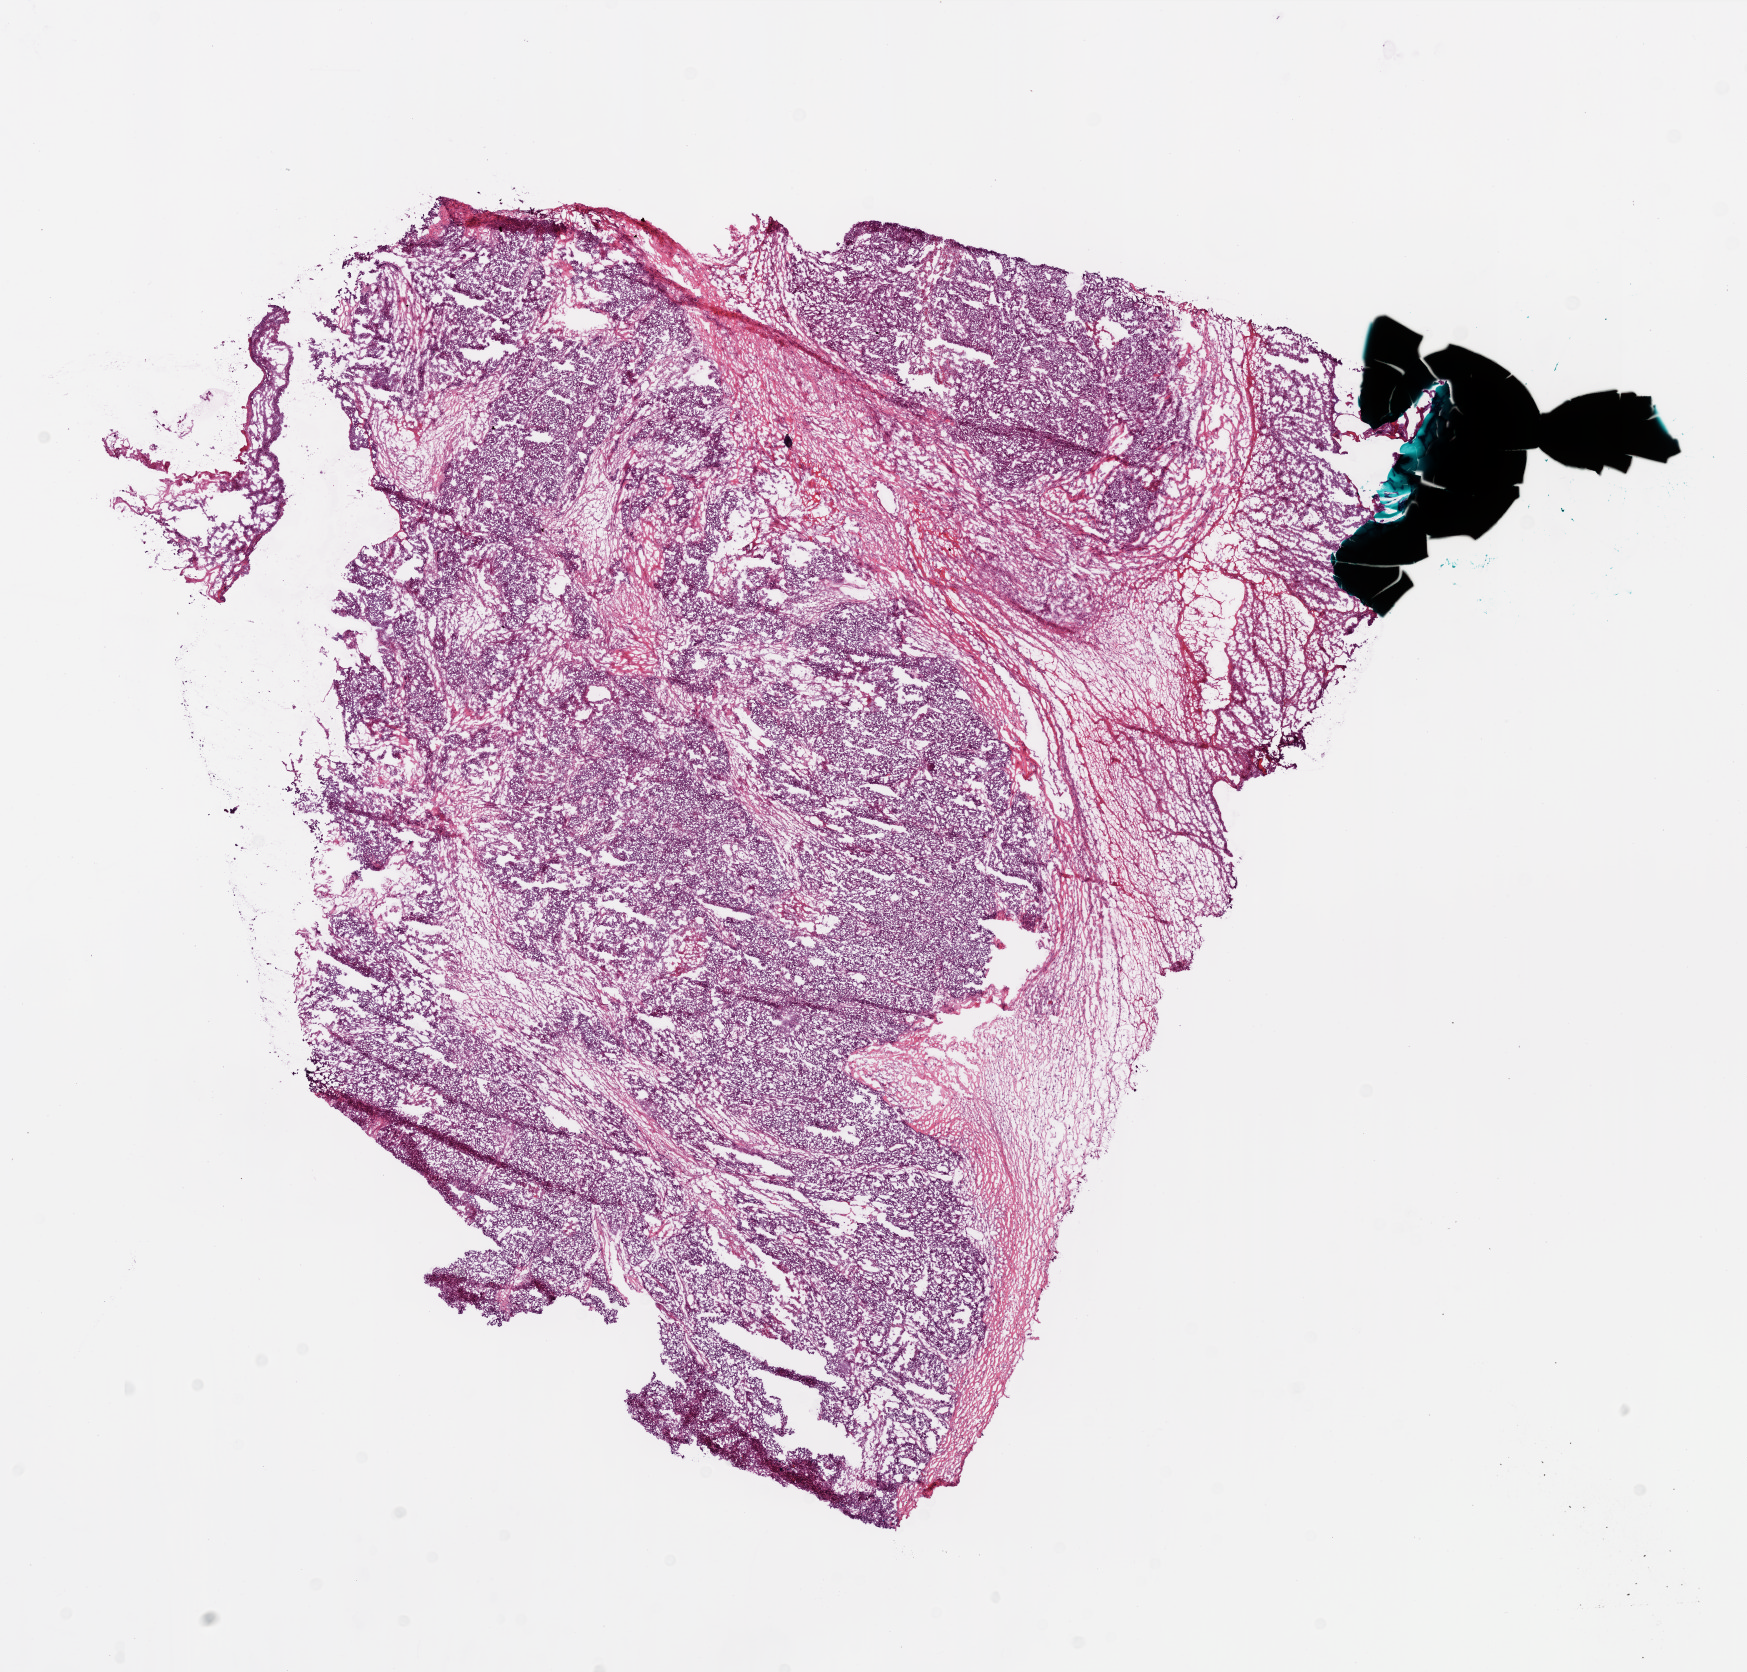
Hematoxylin and eosin (H&E) stained whole-slide image, shown as a low-resolution overview of the whole scanned area (about 14.0 x 13.4 mm, from a 20x scan). Frozen section from the bottom of the tissue portion. Primary tumour sample from the ovary. Female, age 53 years at initial diagnosis. Histologic grade: G3 (poorly differentiated). Composition of this section per pathologist review: tumour cells 80%, tumour nuclei 90%, normal cells 0%, stromal cells 20%, necrosis 0%.
- FIGO stage: IIIC
- diagnosis: Serous cystadenocarcinoma, NOS